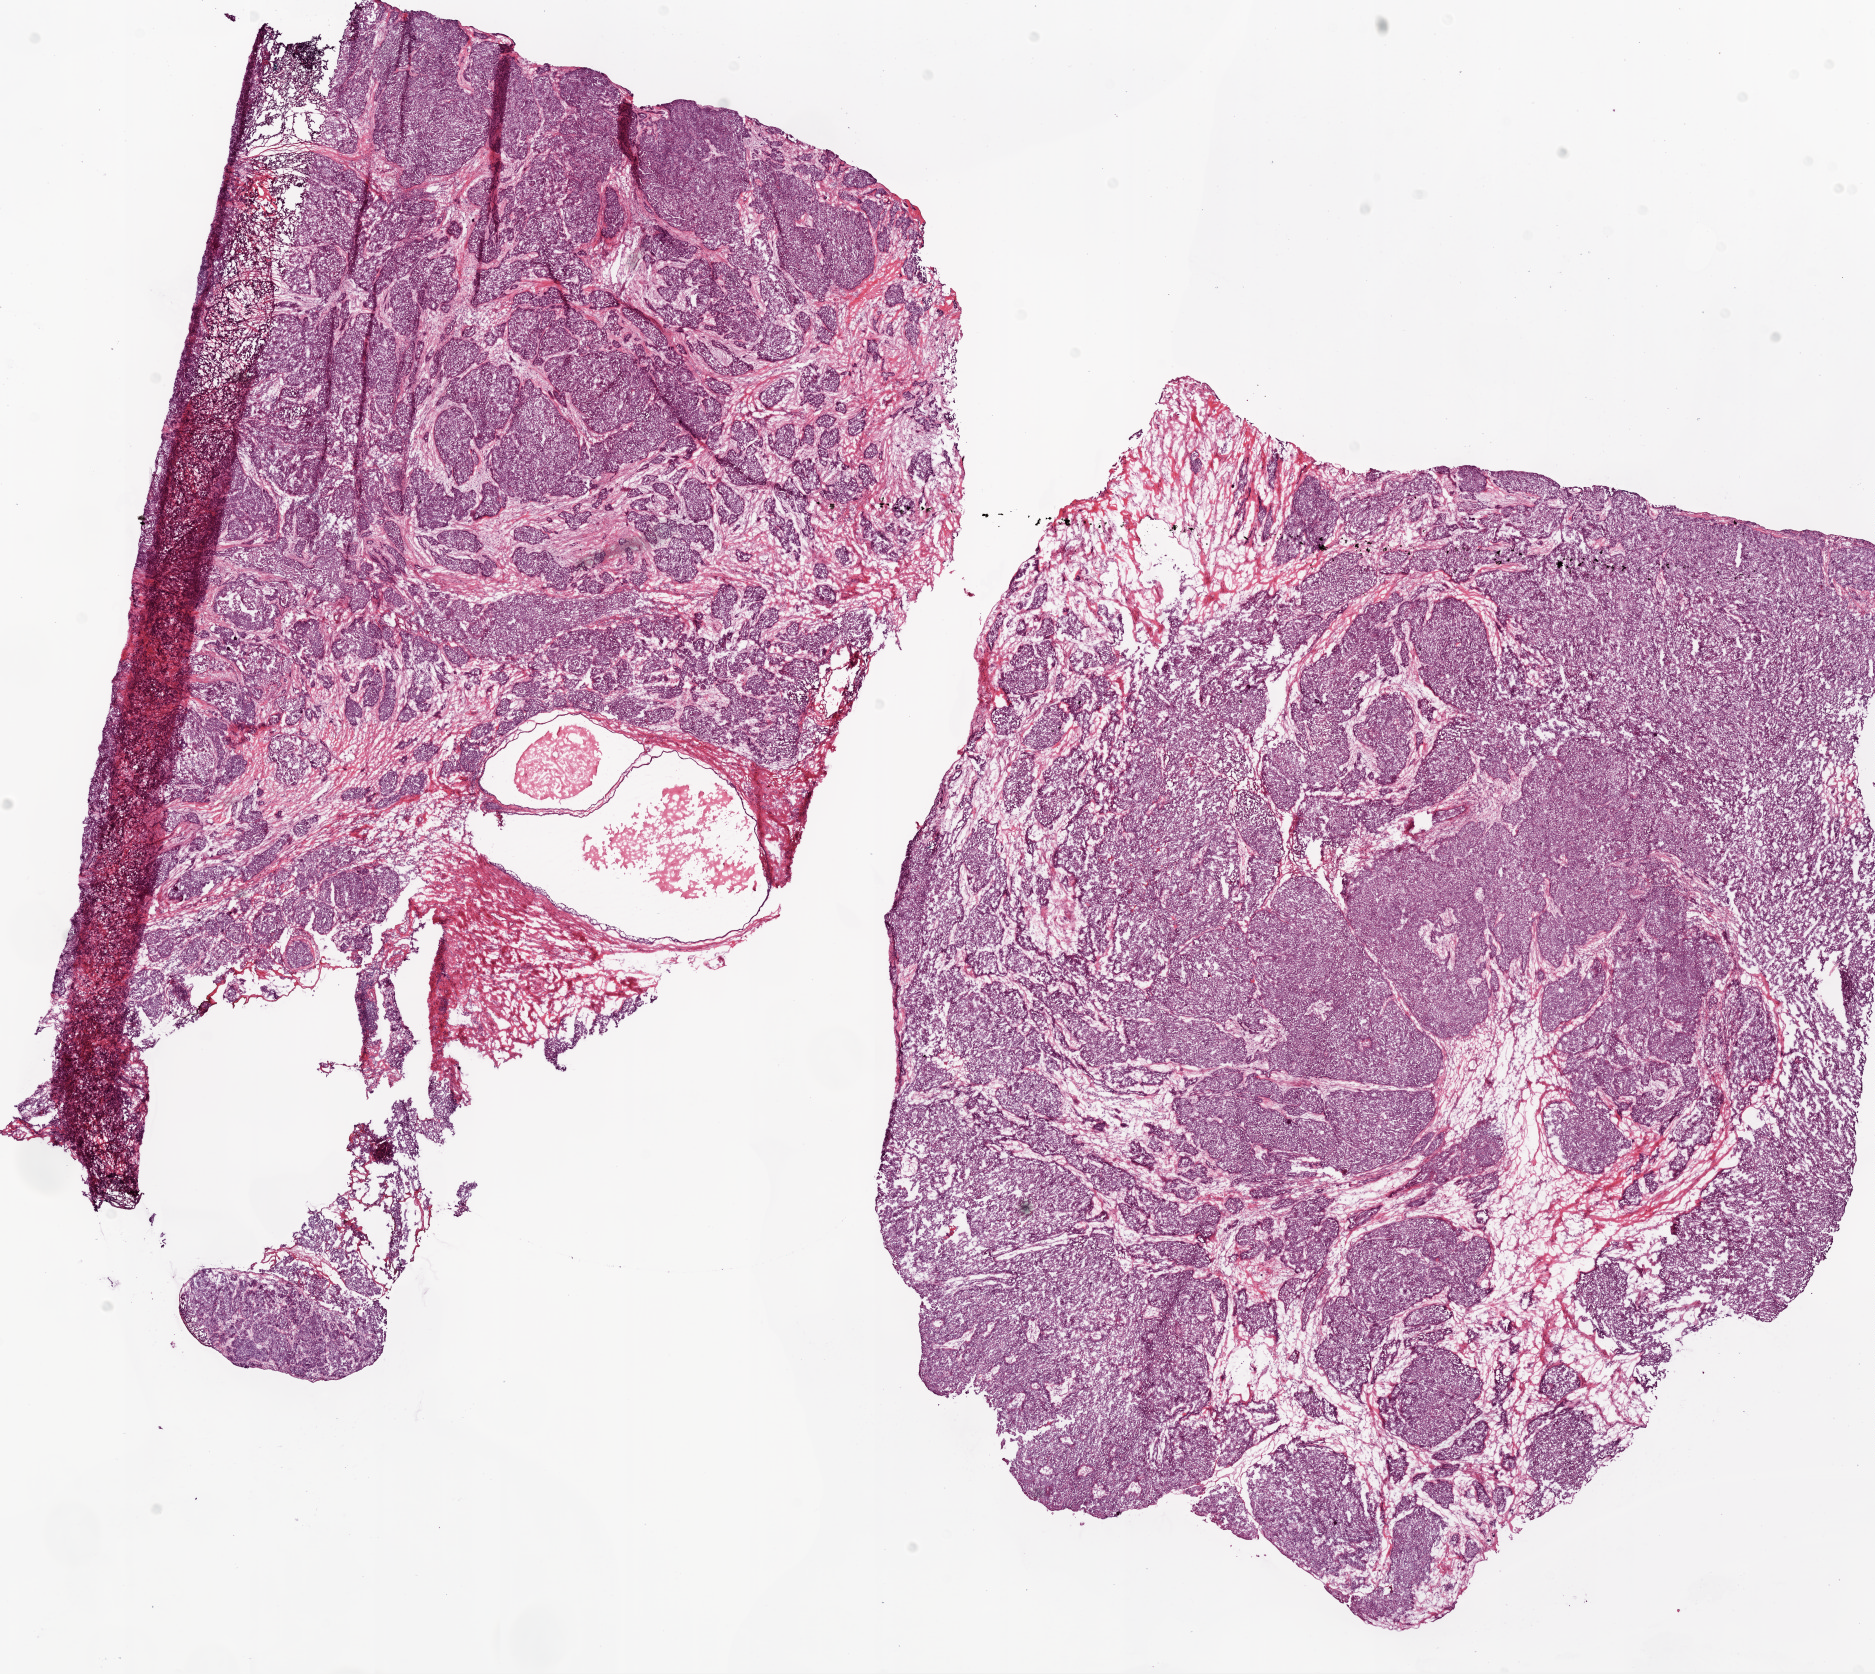
Whole-slide histology image, H&E, whole scanned area (about 15.0 x 13.4 mm, acquisition: 20x scan) shown as a low-resolution overview. Frozen section. Ovary, primary tumour sample. Female, age 46 years at initial diagnosis. Histologic grade: G3 (poorly differentiated). Composition of this section per pathologist review: tumour cells 85%, tumour nuclei 90%, normal cells 0%, stromal cells 15%, necrosis 0%.
• FIGO stage: IV
• laterality: bilateral
• diagnosis: Serous cystadenocarcinoma, NOS